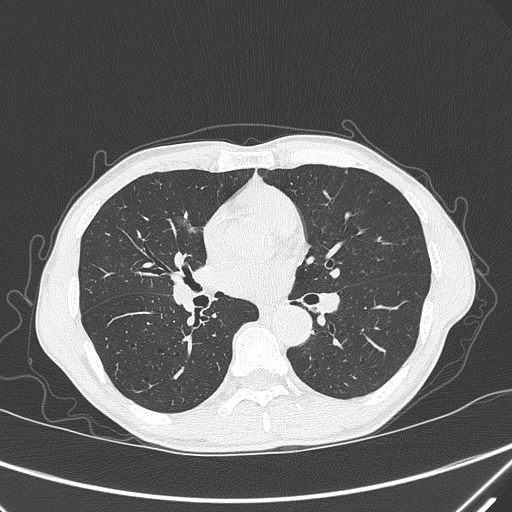
Chest CT, one axial slice. Position 174 of 339 along the scan axis. Lung window (W 1500 / L -600 HU). 1 mm slice thickness. 512 × 512 image matrix, field of view 350 × 350 mm. Male patient, age 67 years. From the clinical record (not read from this slice): clinical TNM (as recorded): T1c N0 M0; histopathological grade: G1-2.
Outlined on this slice (rectangle marked by the reading radiologist):
- lung tumour (recorded histology: adenocarcinoma): bounding box [x1, y1, x2, y2] px = [170, 198, 208, 245]